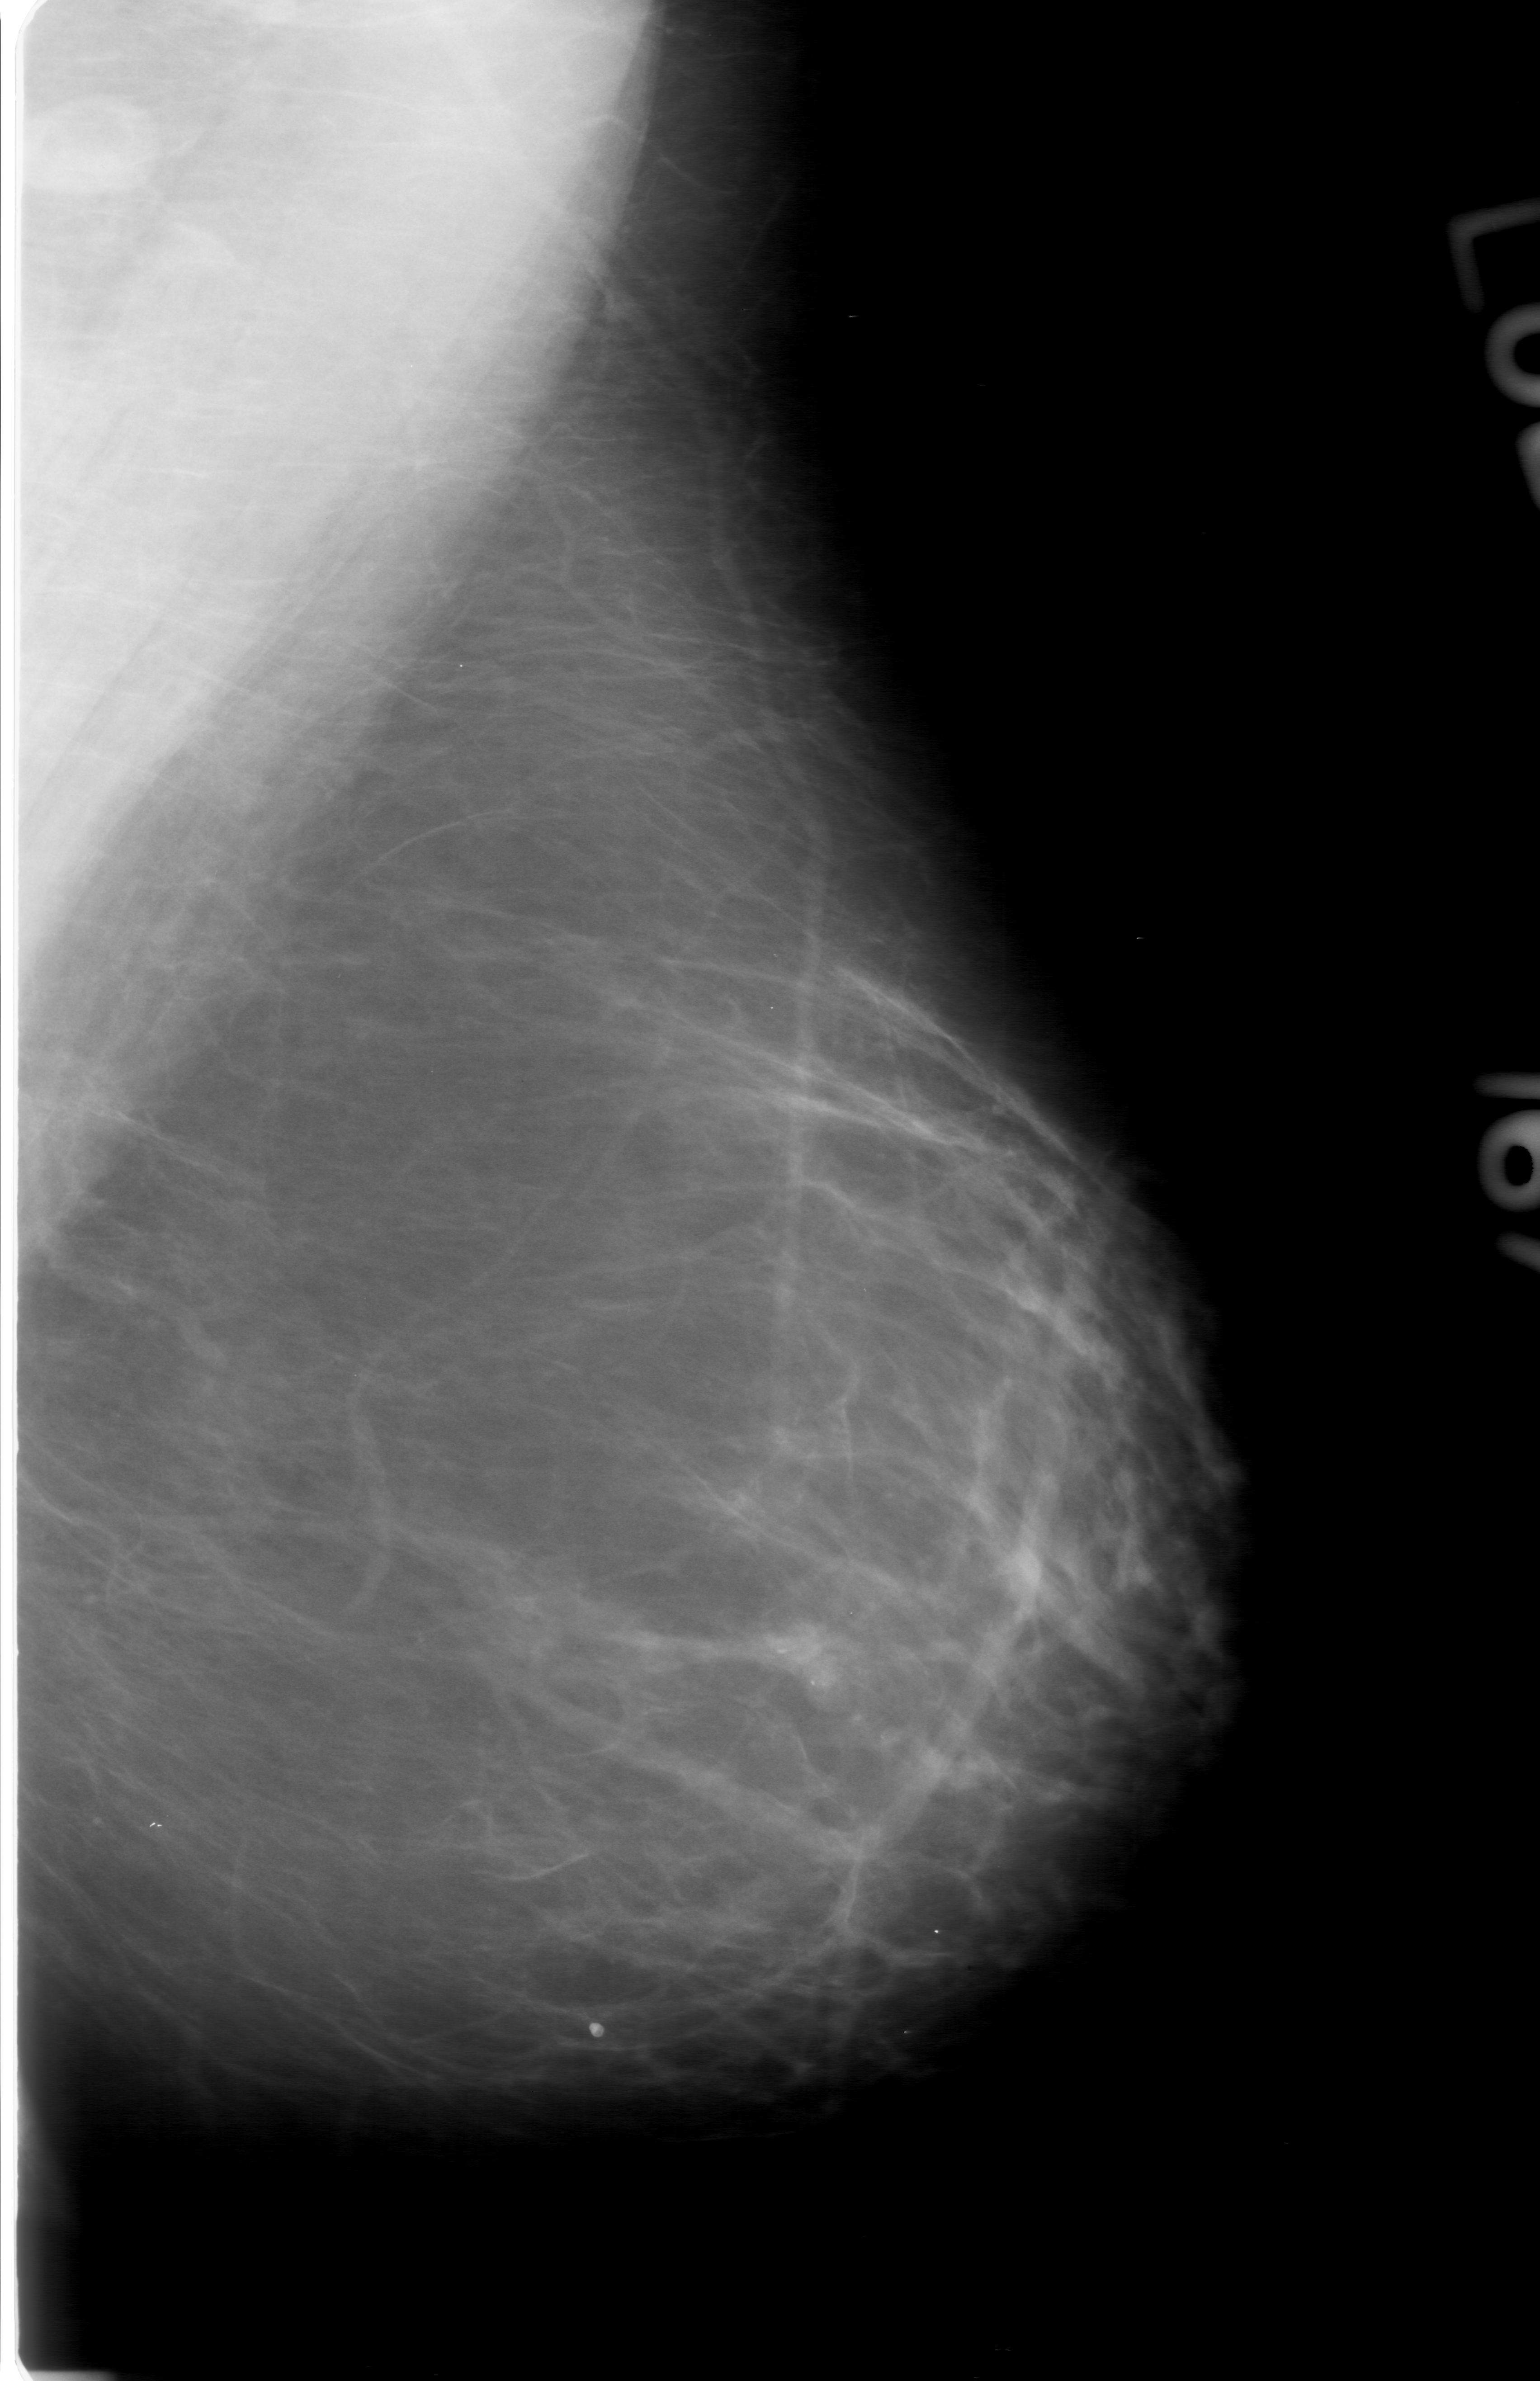
Mammogram (digitized film); left breast; MLO view; BI-RADS breast density category 1 (scale 1–4).
- Marked abnormality: calcifications, morphology fine linear branching, distribution clustered; BI-RADS assessment category 3; pathology result (as recorded, not read from the image): malignant.